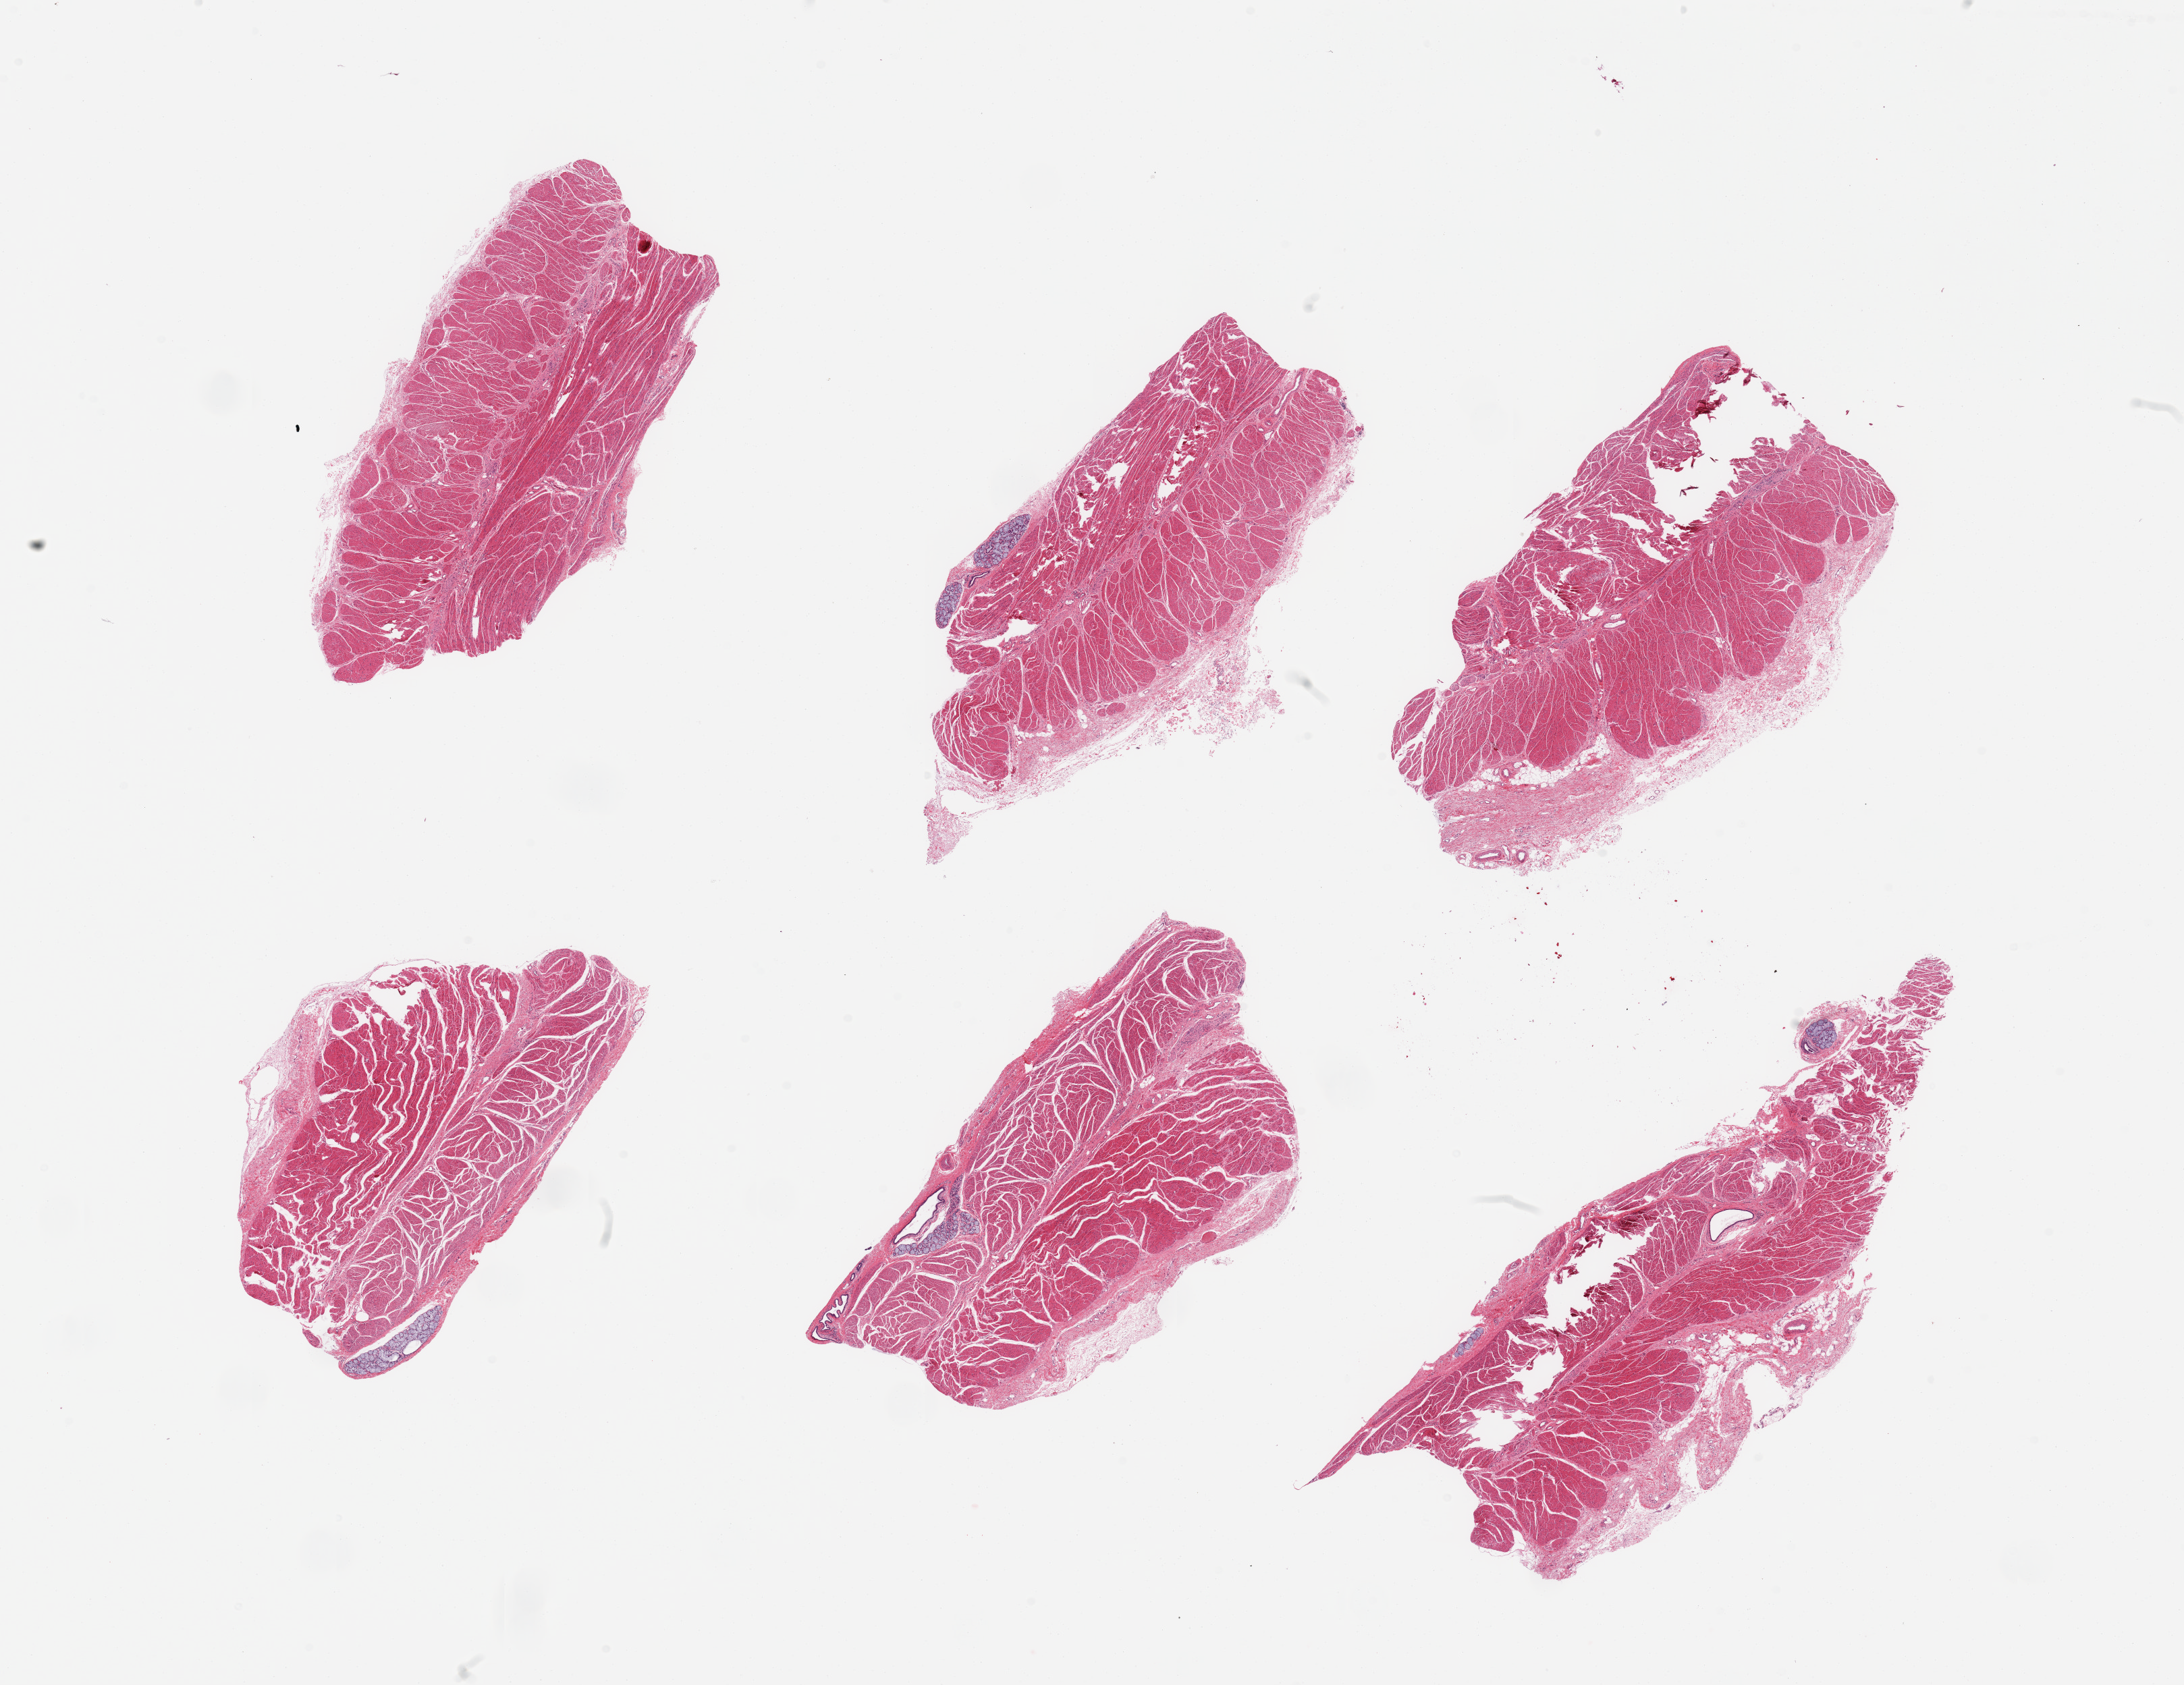
H&E whole-slide image — a low-resolution overview of the entire scanned area, about 25.6 x 19.7 mm; PAXgene-fixed, paraffin-embedded tissue; sampled site (target tissue): gastroesophageal junction; donor tissue sample. Donor sex: male.
Pathologist's review note for this sample: 6 pieces; target muscularis with few clusters of submucosal glands.